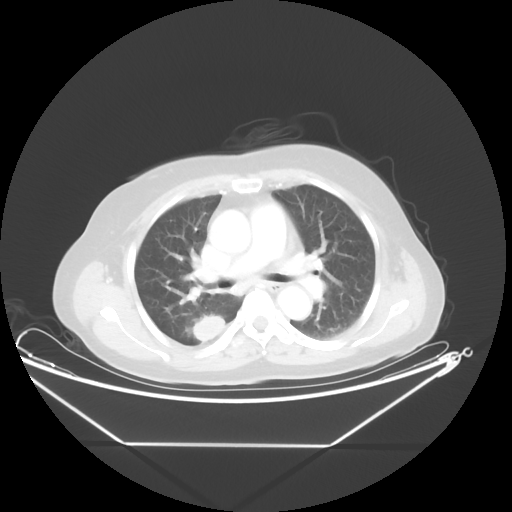
Chest CT, one axial slice. Position 28 of 48 along the scan axis. Reconstruction kernel STANDARD. 100 kVp. Lung window (W 1500 / L -600 HU). 5 mm slice thickness. 512 × 512 image matrix, field of view 462 × 462 mm. Patient: female, 62 years. Case-level facts recorded for this patient, not image findings: clinical TNM (as recorded): T1c N0 M0.
Annotated regions visible in this slice (bounding box drawn by a radiologist):
- lung tumour (recorded histology: adenocarcinoma): bounding box (x1, y1, x2, y2) in pixels: (187, 309, 232, 350)